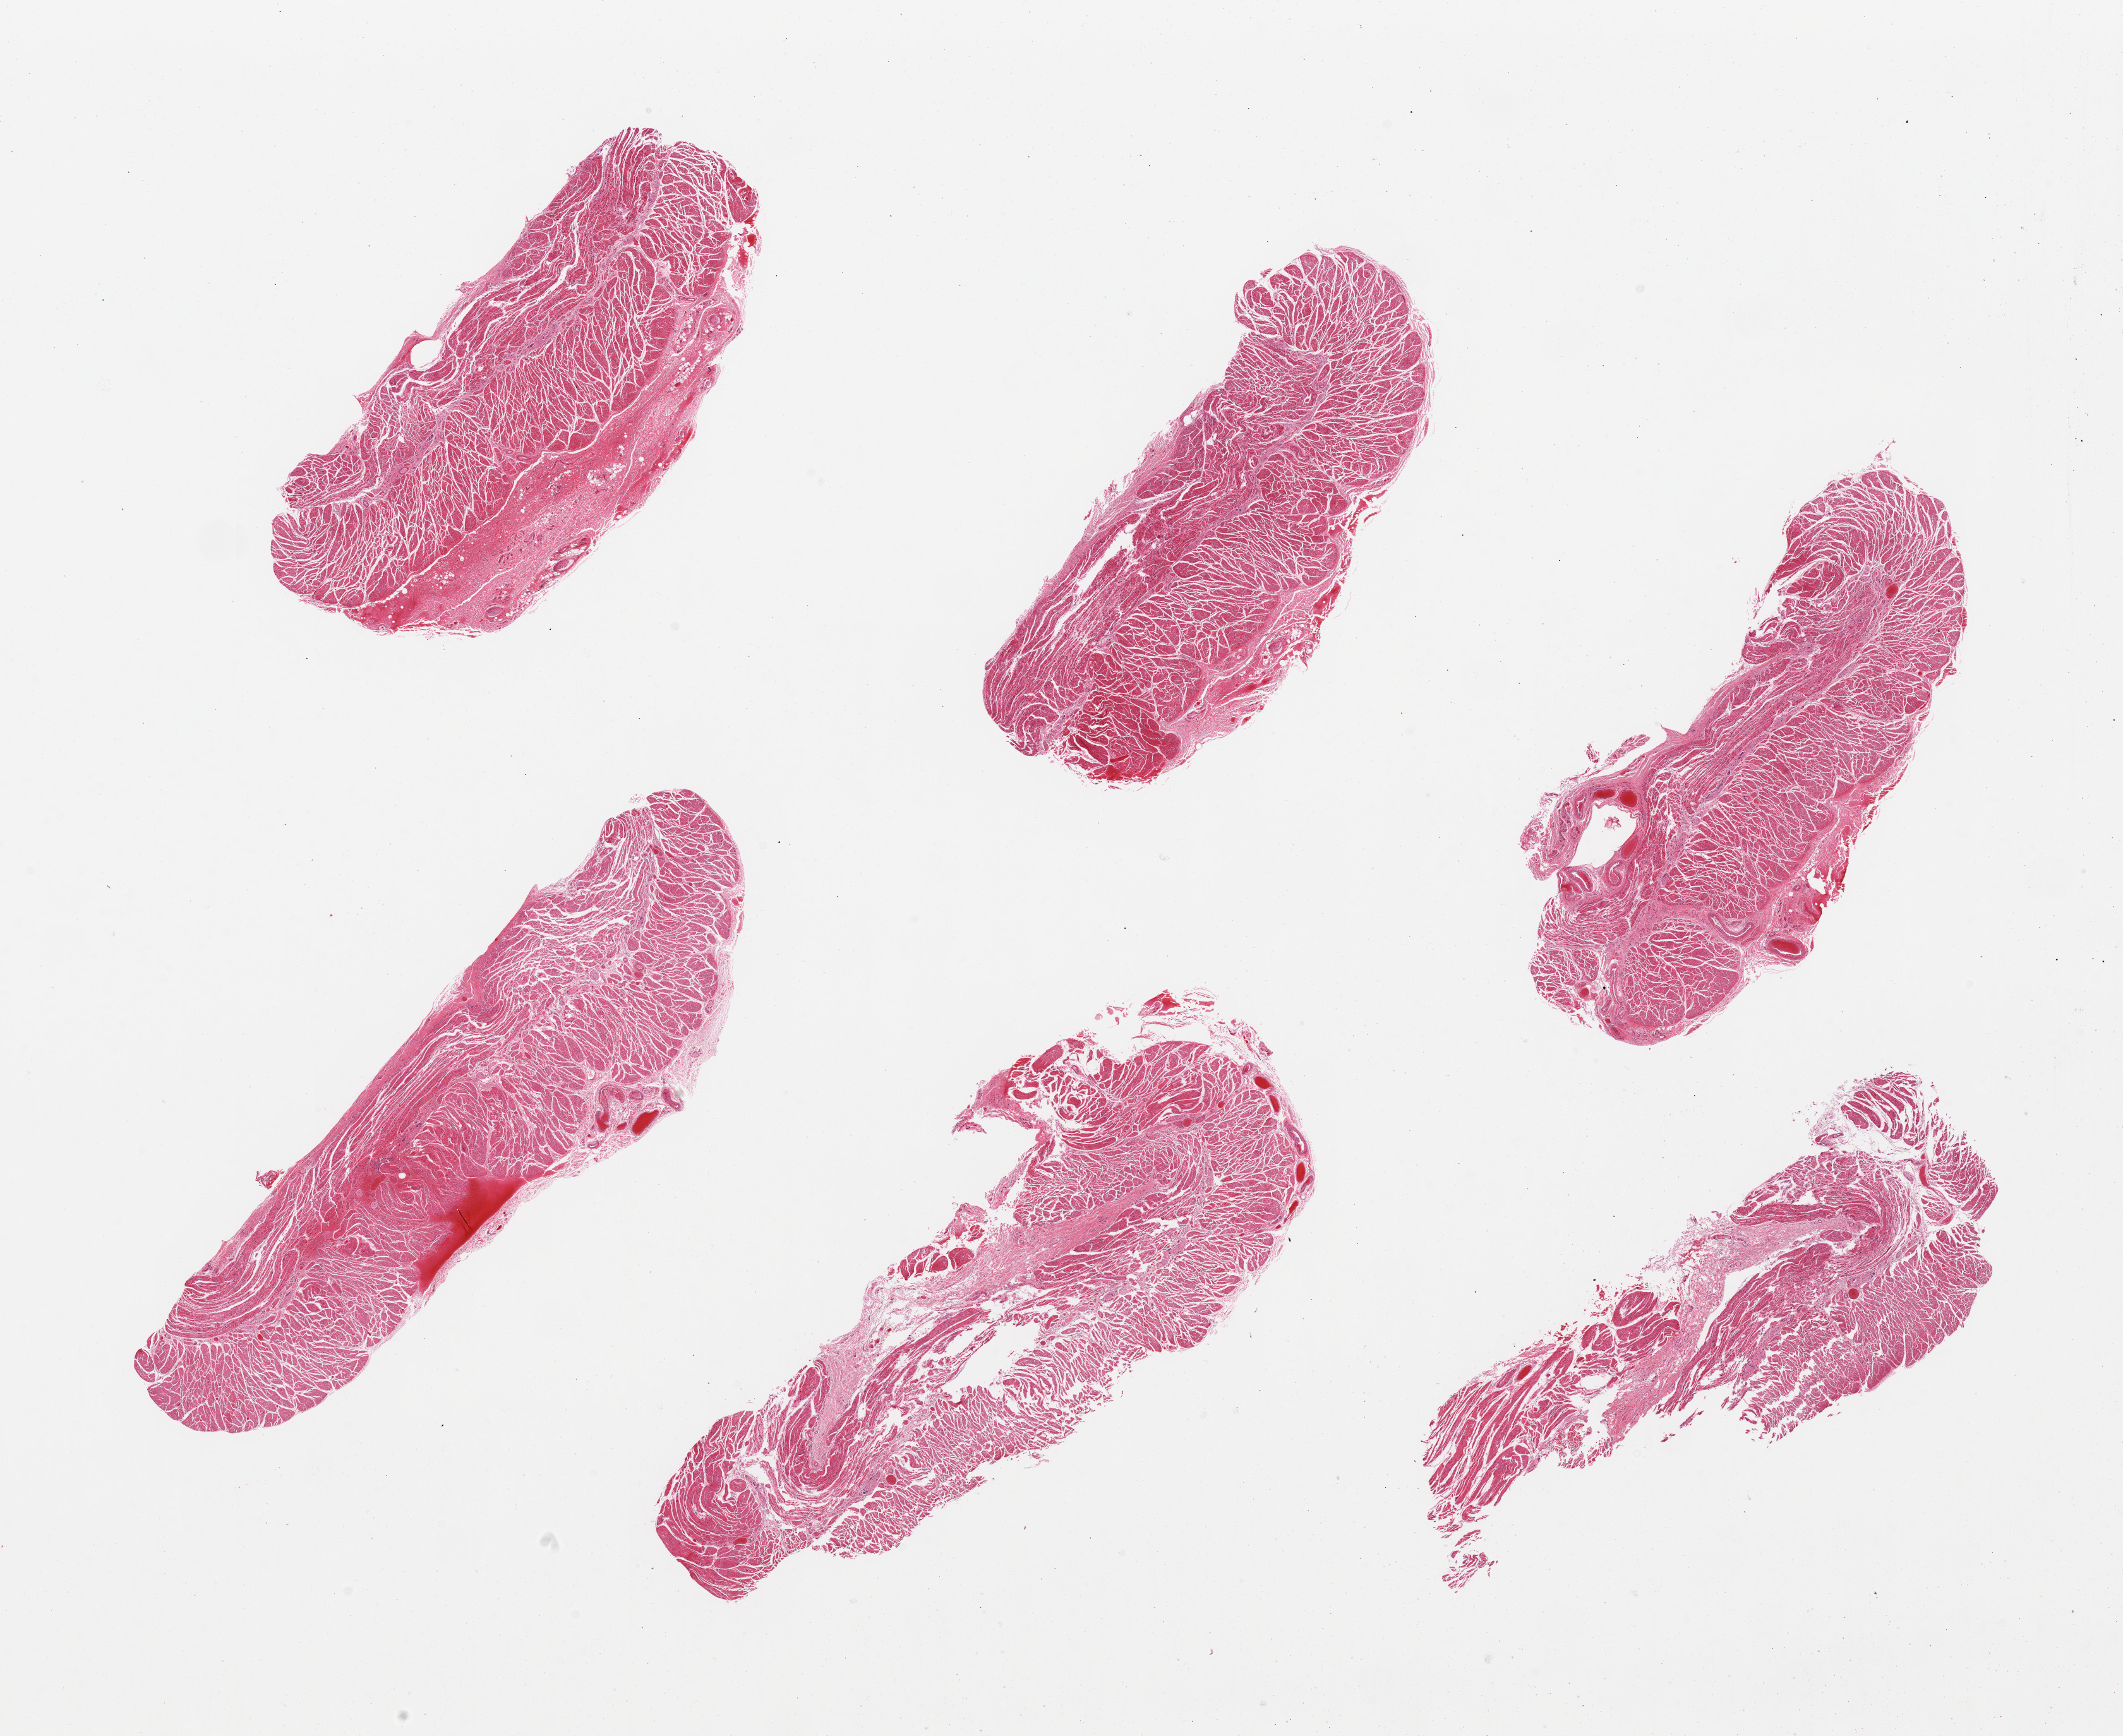
Hematoxylin and eosin (H&E) whole-slide image, brightfield — a low-resolution overview of the entire scanned area, about 26.6 x 21.7 mm. PAXgene-fixed paraffin-embedded (PFPE) section. Target tissue: esophageal muscle. Tissue donor sample. Female donor.
* review note (as recorded): 6 pieces